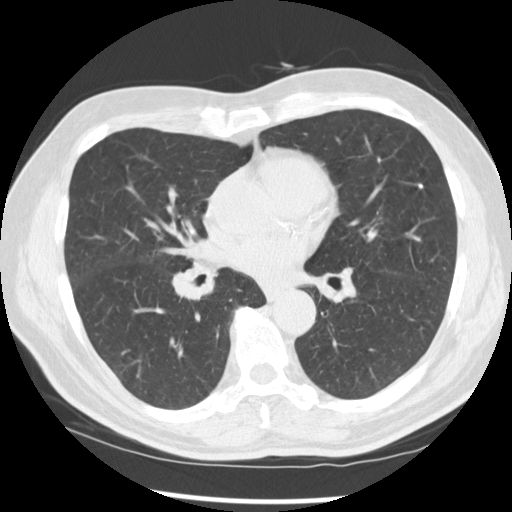
Low-dose screening chest CT, one axial slice; position 141 of 277 along the scan axis; reconstruction kernel STANDARD; 120 kVp; lung window (W 1500 / L -600 HU); 512 × 512 image matrix.
Annotated regions visible in this slice (expert manual segmentation):
- lesion 1 (tumor, middle lobe of right lung): box from (x=172, y=264) to (x=215, y=301) px